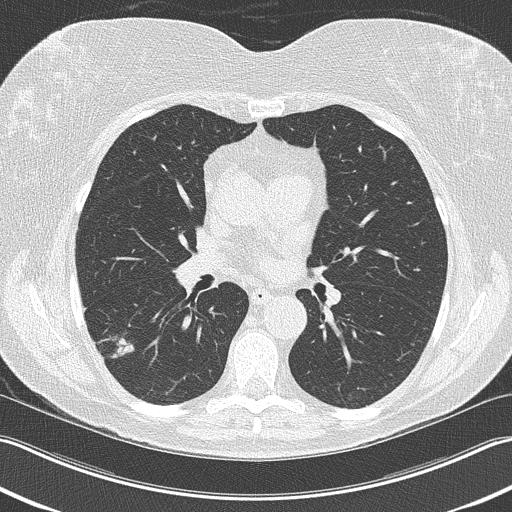
Low-dose screening chest CT, one axial slice. Slice 124 of 210 in the series (ordered by position). 120 kVp. Lung window (W 1500 / L -600 HU). 512 × 512 image matrix.
Outlined on this slice (manually delineated by an expert):
- lesion 1 (tumor, lower lobe of right lung): bounding box <111,338,134,358> (left, top, right, bottom; pixels)